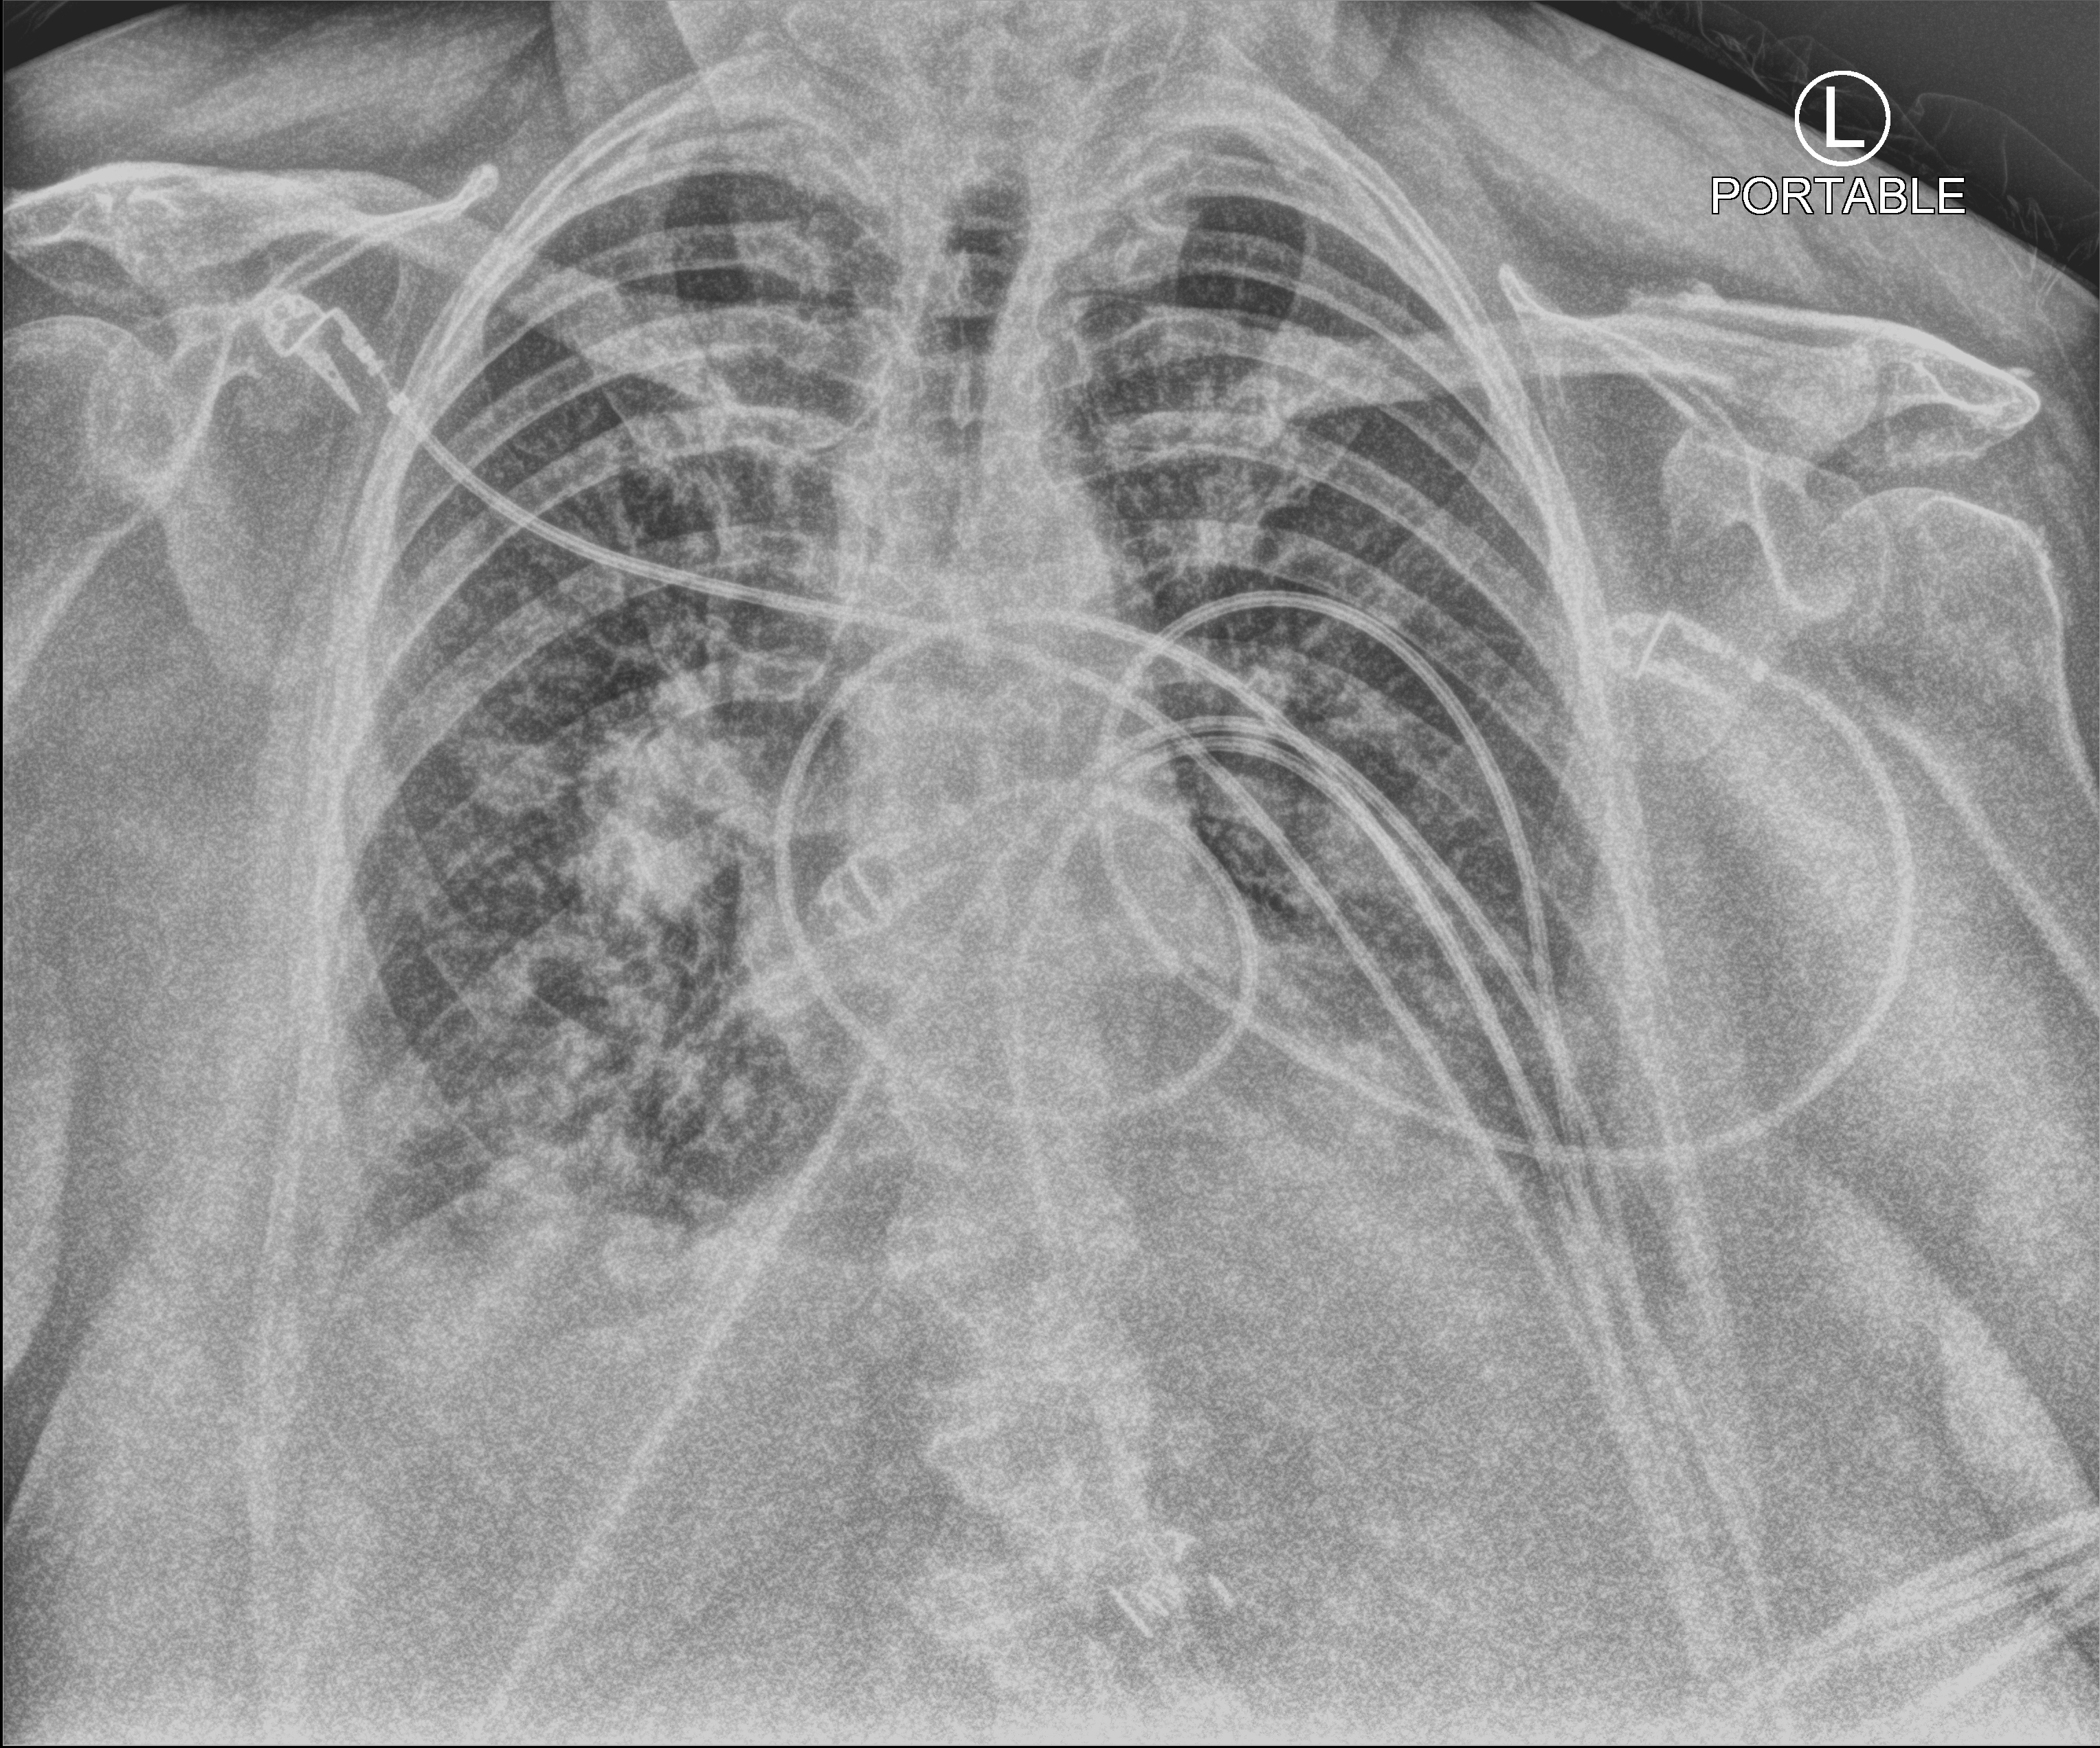
Chest X-ray (portable), anteroposterior (AP) projection. Female patient hospitalised with COVID-19, age 75–90 years.
Admission-level facts for this patient (not findings on this image; timing relative to this image not recorded): hypertension (admission record): yes; length of hospital stay: 19 days; admitted to intensive care during this hospital stay: no.